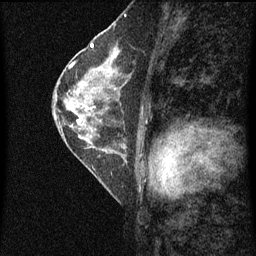
Breast MRI (dynamic contrast-enhanced), one sagittal slice. Dynamic contrast-enhanced series, image 2 of 4 at this slice position (ordered by acquisition). 1.5 T. TE 4.2 ms, TR 8 ms. 2 mm slice thickness. 256 × 256 image matrix. Patient: female, 56 years.
Outlined on this slice (semi-automatically segmented with operator editing):
- analysis volume of interest (the breast-tissue region the enhancement analysis was run in; not a lesion): box from (x=56, y=52) to (x=122, y=115) px
- tumour enhancement mask (voxels above the 70 % enhancement threshold inside the analysis volume of interest): (x=84, y=56)–(x=117, y=109)